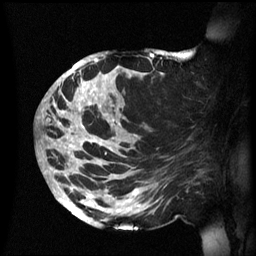
Breast MRI (dynamic contrast-enhanced), one sagittal slice. Slice 32 of 60 in the series (ordered by position). Dynamic contrast-enhanced series, image 2 of 3 at this slice position (ordered by acquisition). 1.5 T. TE 4.2 ms, TR 8.4 ms. 2.4 mm slice thickness. 256 × 256 image matrix, field of view 230 × 230 mm. Female patient, age 48 years.
Annotated regions visible in this slice (semi-automatic segmentation, software-assisted and operator-edited):
- analysis volume of interest (the breast-tissue region the enhancement analysis was run in; not a lesion): box from (x=42, y=49) to (x=200, y=231) px
- tumour enhancement mask (voxels above the 70 % enhancement threshold inside the analysis volume of interest): (x=42, y=52)–(x=175, y=222)